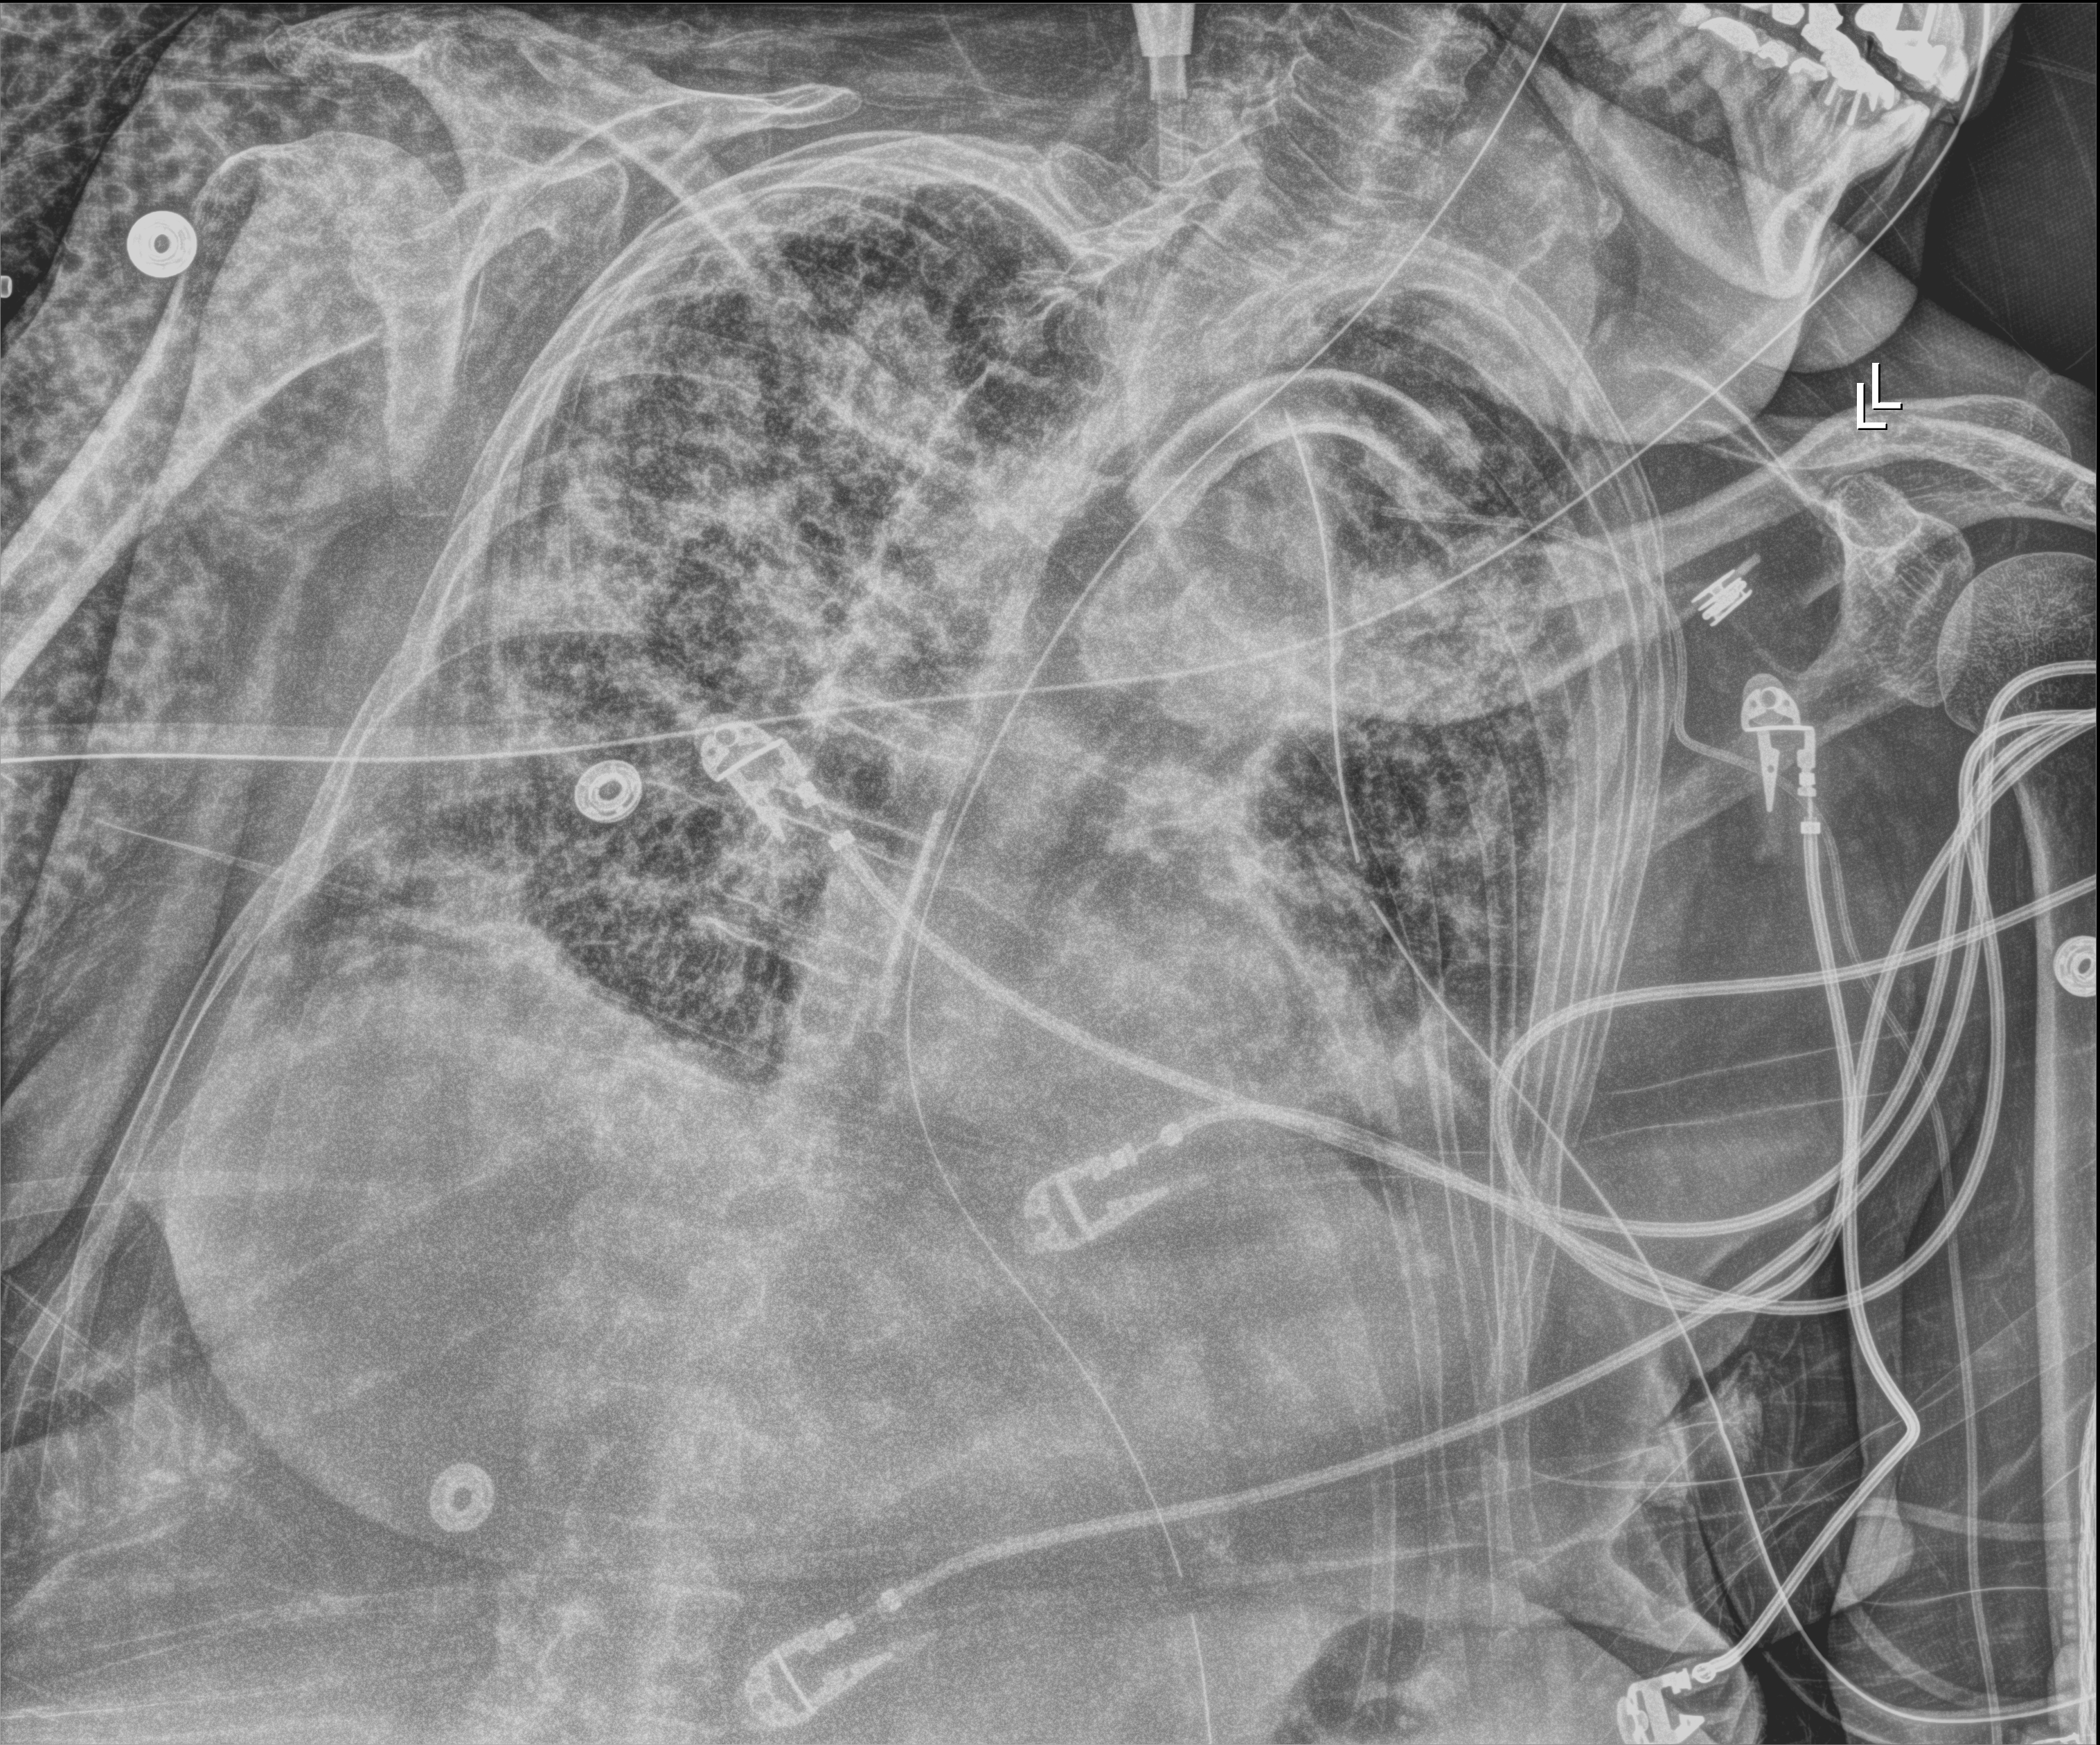
Bedside chest radiograph (digital radiography), anteroposterior (AP) projection. Female patient hospitalised with COVID-19, age 75–90 years.
From the hospital-stay record, not from the radiograph (when in the stay this image was taken is not recorded): mechanically ventilated during this hospital stay: yes; admitted to intensive care during this hospital stay: yes.